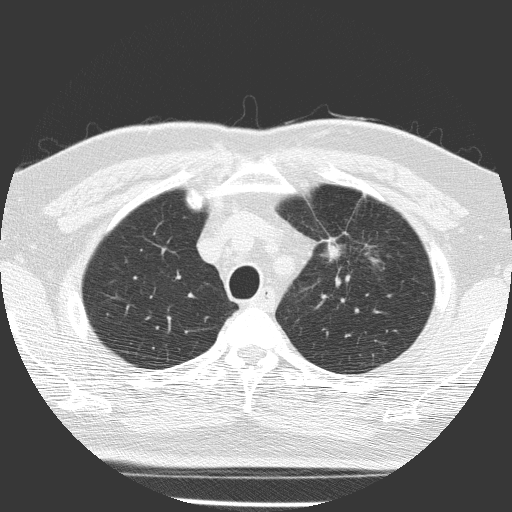
Low-dose screening chest CT, one axial slice. Position 122 of 156 along the scan axis. Lung window (W 1500 / L -600 HU). 2 mm slice thickness. 512 × 512 image matrix, field of view 309 × 309 mm.
Outlined on this slice (outlined manually by an expert reader):
- lesion 1 (tumor, upper lobe of left lung): bounding box (x1, y1, x2, y2) in pixels: (325, 242, 341, 260)